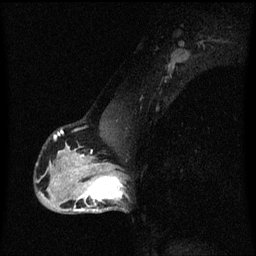
Breast MRI (dynamic contrast-enhanced), one sagittal slice; position 38 of 60 along the scan axis; dynamic contrast-enhanced series, image 2 of 3 at this slice position (ordered by acquisition); 1.5 T; TE 4.2 ms, TR 8.4 ms; 2 mm slice thickness; 256 × 256 image matrix, field of view 200 × 200 mm. Female patient, age 40 years.
Structures marked on this image (semi-automatically segmented with operator editing):
- analysis volume of interest (the breast-tissue region the enhancement analysis was run in; not a lesion): bounding box <76,172,128,213> (left, top, right, bottom; pixels)
- tumour enhancement mask (voxels above the 70 % enhancement threshold inside the analysis volume of interest): <76,172,124,211>